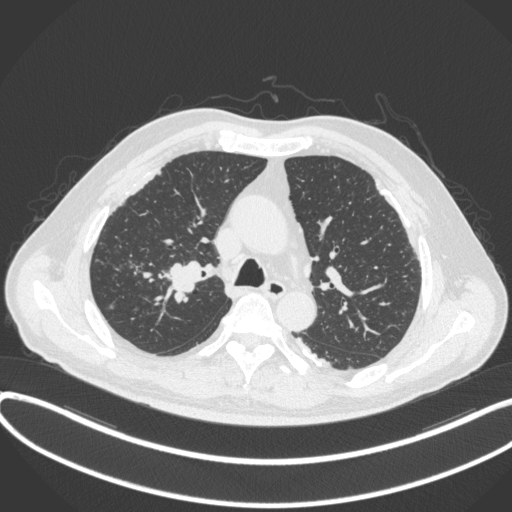
Chest CT, one axial slice; position 289 of 455 along the scan axis; lung window (W 1500 / L -600 HU); 512 × 512 image matrix, field of view 400 × 400 mm. Patient: male, 58 years. From the clinical record (not read from this slice): clinical TNM (as recorded): T1c N0 M0.
Annotated regions visible in this slice (rectangle marked by the reading radiologist):
- lung tumour (recorded histology: squamous cell carcinoma): bounding box (x1, y1, x2, y2) in pixels: (163, 257, 206, 301)